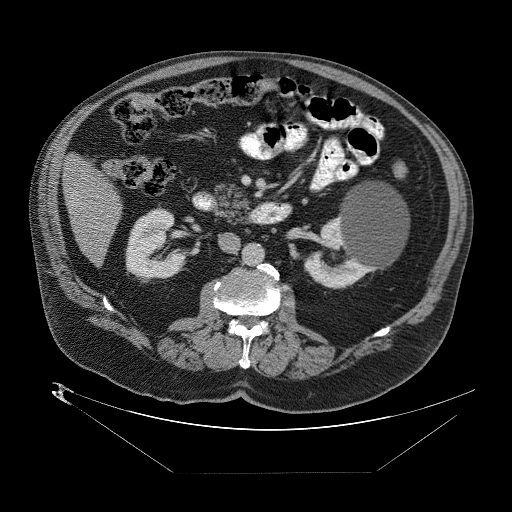
Contrast-enhanced abdominal CT (liver protocol), one axial slice; position 15 of 89 along the scan axis; 140 kVp; one of 2 acquisitions stored at this slice position; soft-tissue window (W 400 / L 40 HU); 2.5 mm slice thickness; 512 × 512 image matrix, field of view 480 × 480 mm. Case-level facts recorded for this patient, not image findings: diagnosis: hepatocellular carcinoma (patient treated with transarterial chemoembolisation; whether this scan precedes or follows treatment is not stated here); TNM stage (as recorded): Stage-II; Child-Pugh class: B; tumour nodularity: multinodular; tumour size: 4 cm.
Annotated regions visible in this slice (semi-automatic segmentation, software-assisted and operator-edited):
- abdominal aorta: bounding box [x1, y1, x2, y2] px = [244, 243, 265, 266]
- liver parenchyma outside the tumour (the mass and vessels are separate outlines, so this box may not span the whole liver): [62, 150, 120, 260]
- liver vessels: [71, 190, 77, 202]